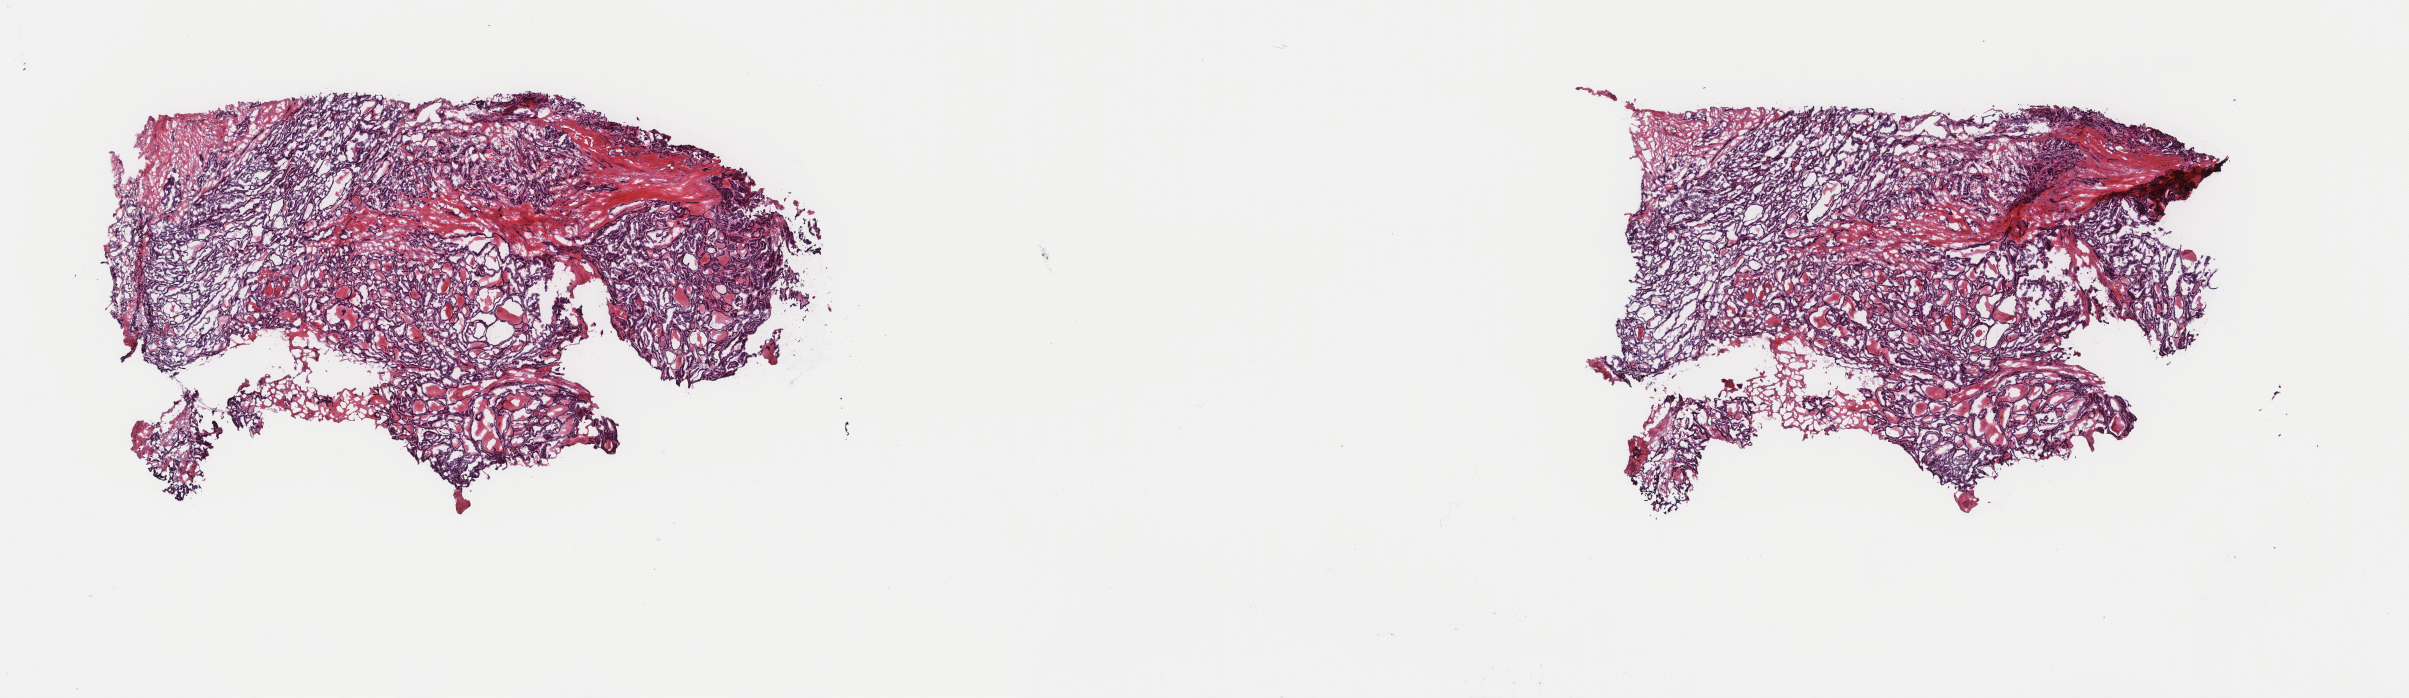
Hematoxylin and eosin (H&E) stained whole-slide image, whole scanned area (about 19.1 x 5.5 mm) shown as a low-resolution overview. Frozen section from the top of the tissue portion. Thyroid, primary tumour sample. Patient: female, age at initial diagnosis 49 years. Slide review estimates, as recorded: tumour cells 75%, tumour nuclei 80%, normal cells 0%, stromal cells 25%, necrosis 0%. Infiltration values recorded for this section: lymphocyte infiltration 2%, monocyte infiltration 1%, neutrophil infiltration 0%.
AJCC pathologic stage: IVA (7th edition). TNM: T1b N1b MX. Pathologic diagnosis: Papillary adenocarcinoma, NOS (thyroid gland).